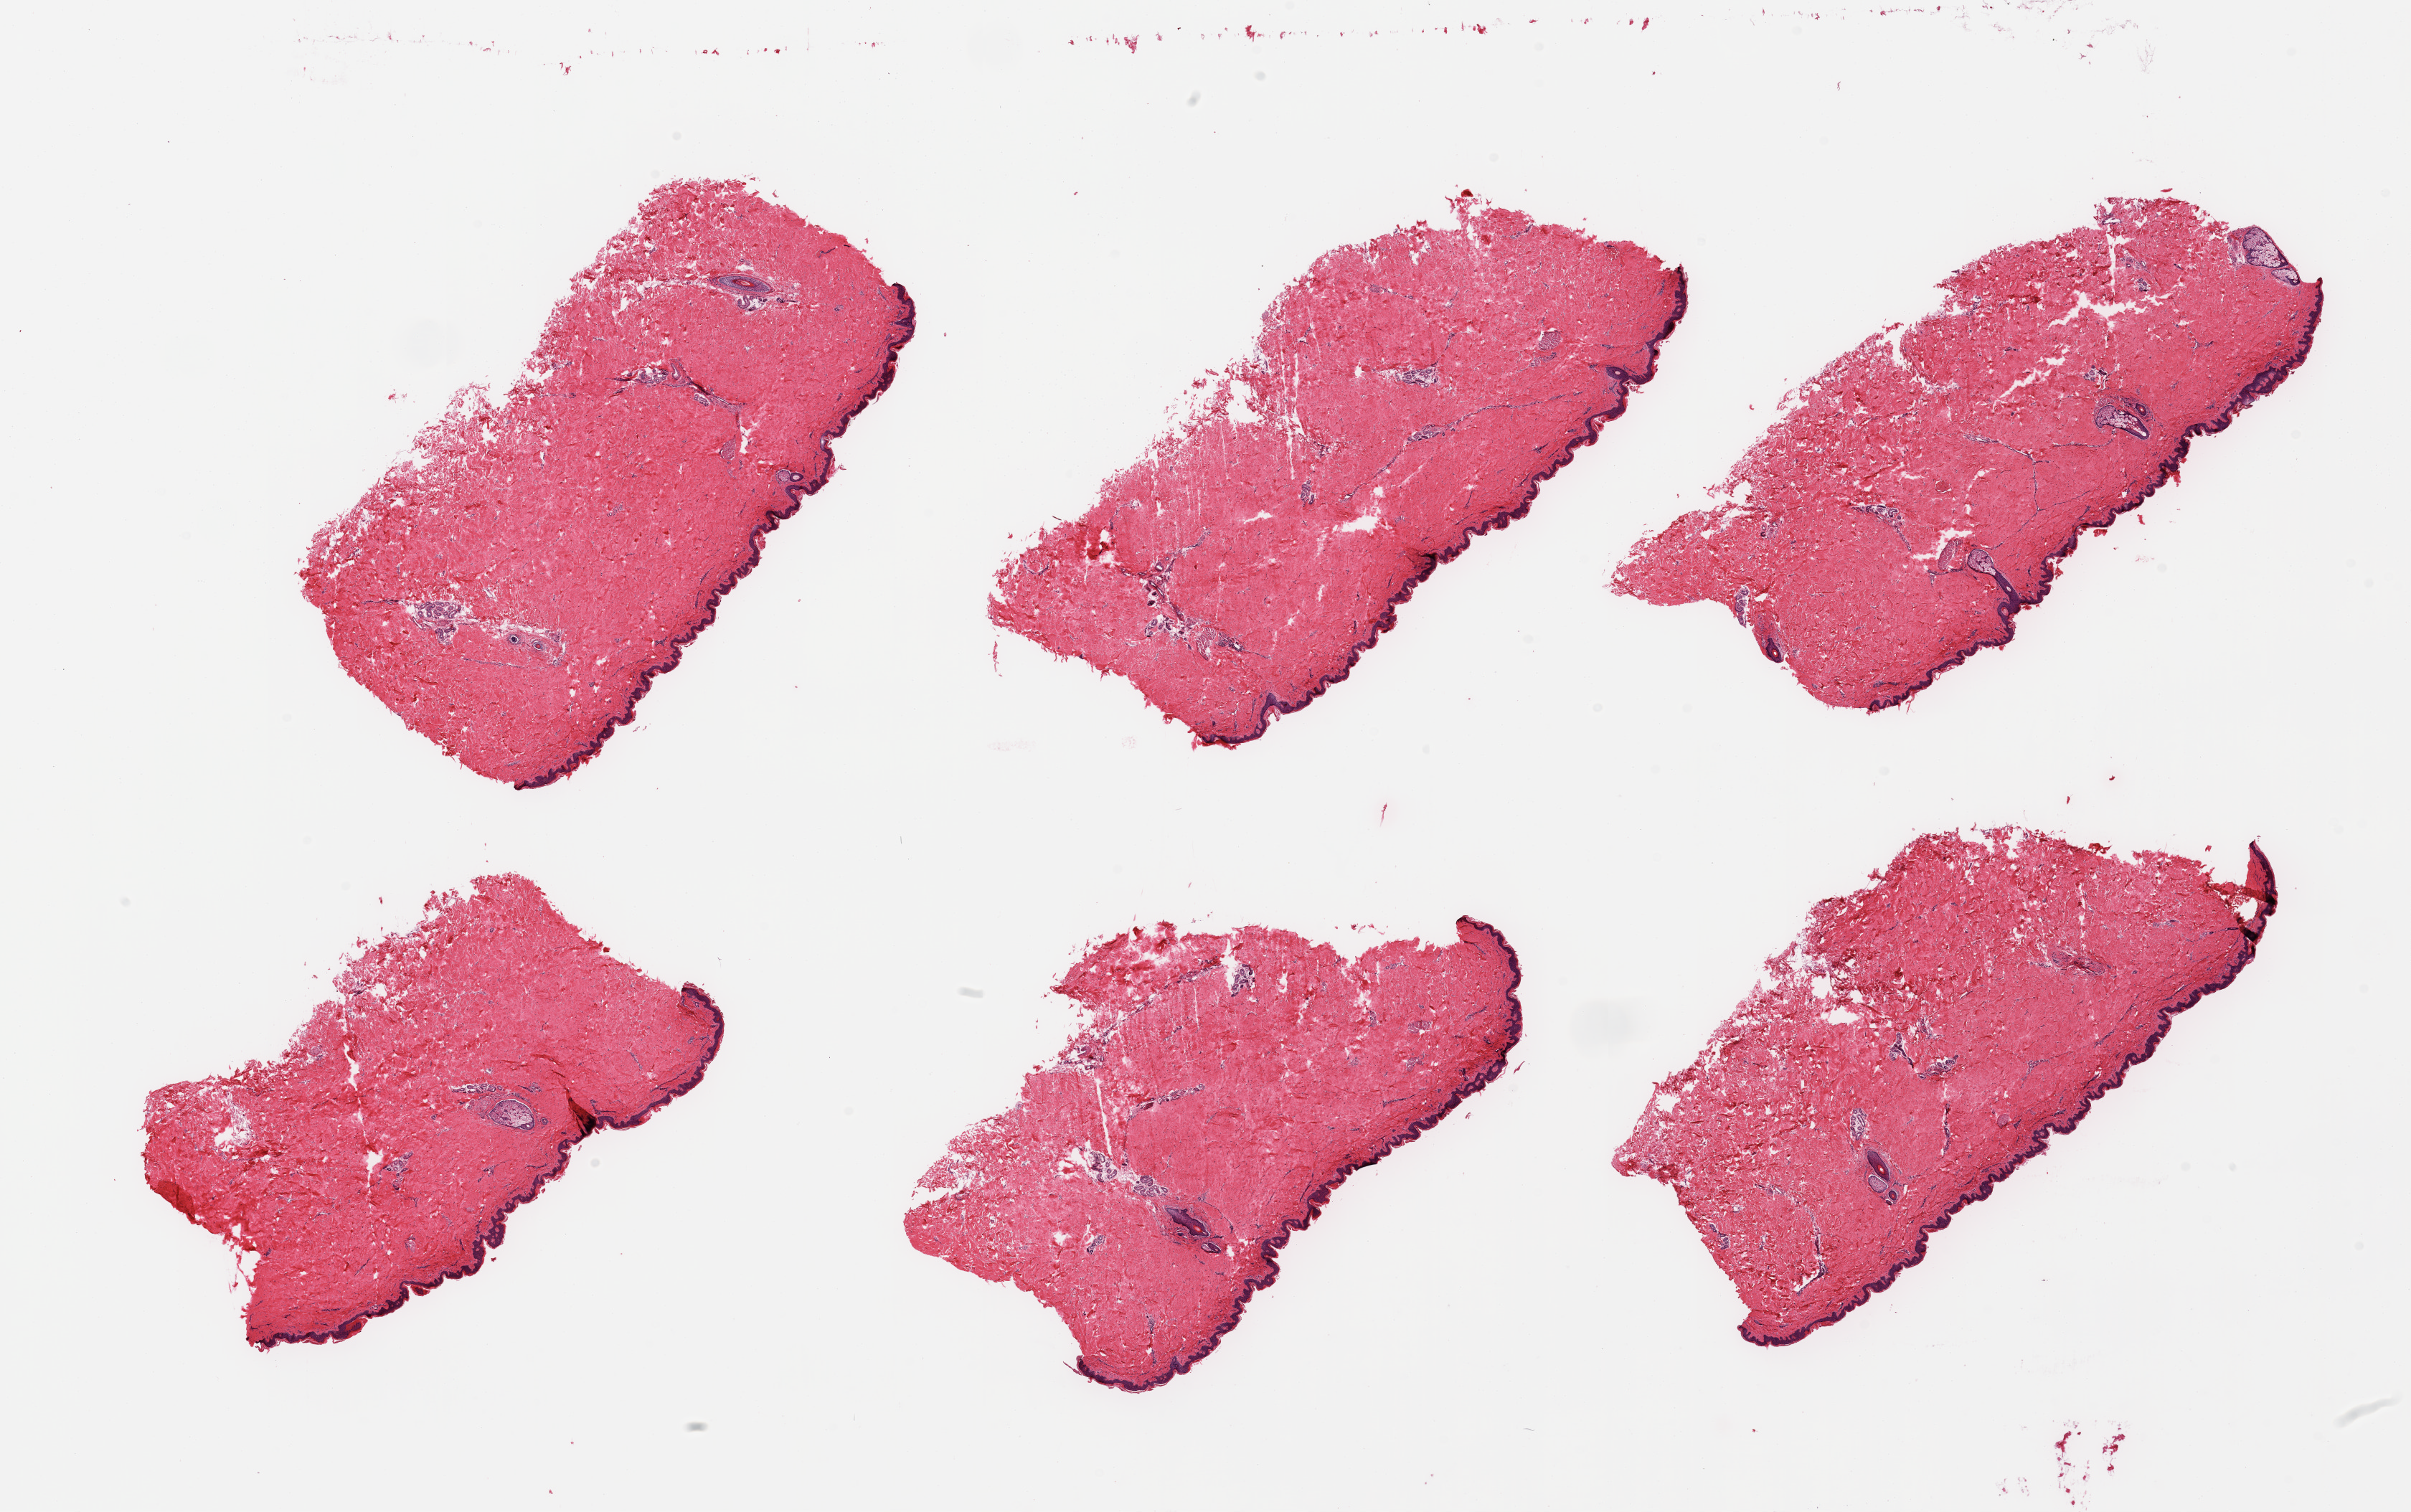
Whole-slide image, hematoxylin and eosin (H&E) stain, brightfield — low-resolution overview of the scanned area, about 26.6 x 16.7 mm, PAXgene-fixed, paraffin-embedded tissue, target tissue: skin of suprapubic region, donor tissue sample. Female donor.
Pathologist's review note for this sample: 6 pieces; well dissected; dermal fat <5%.